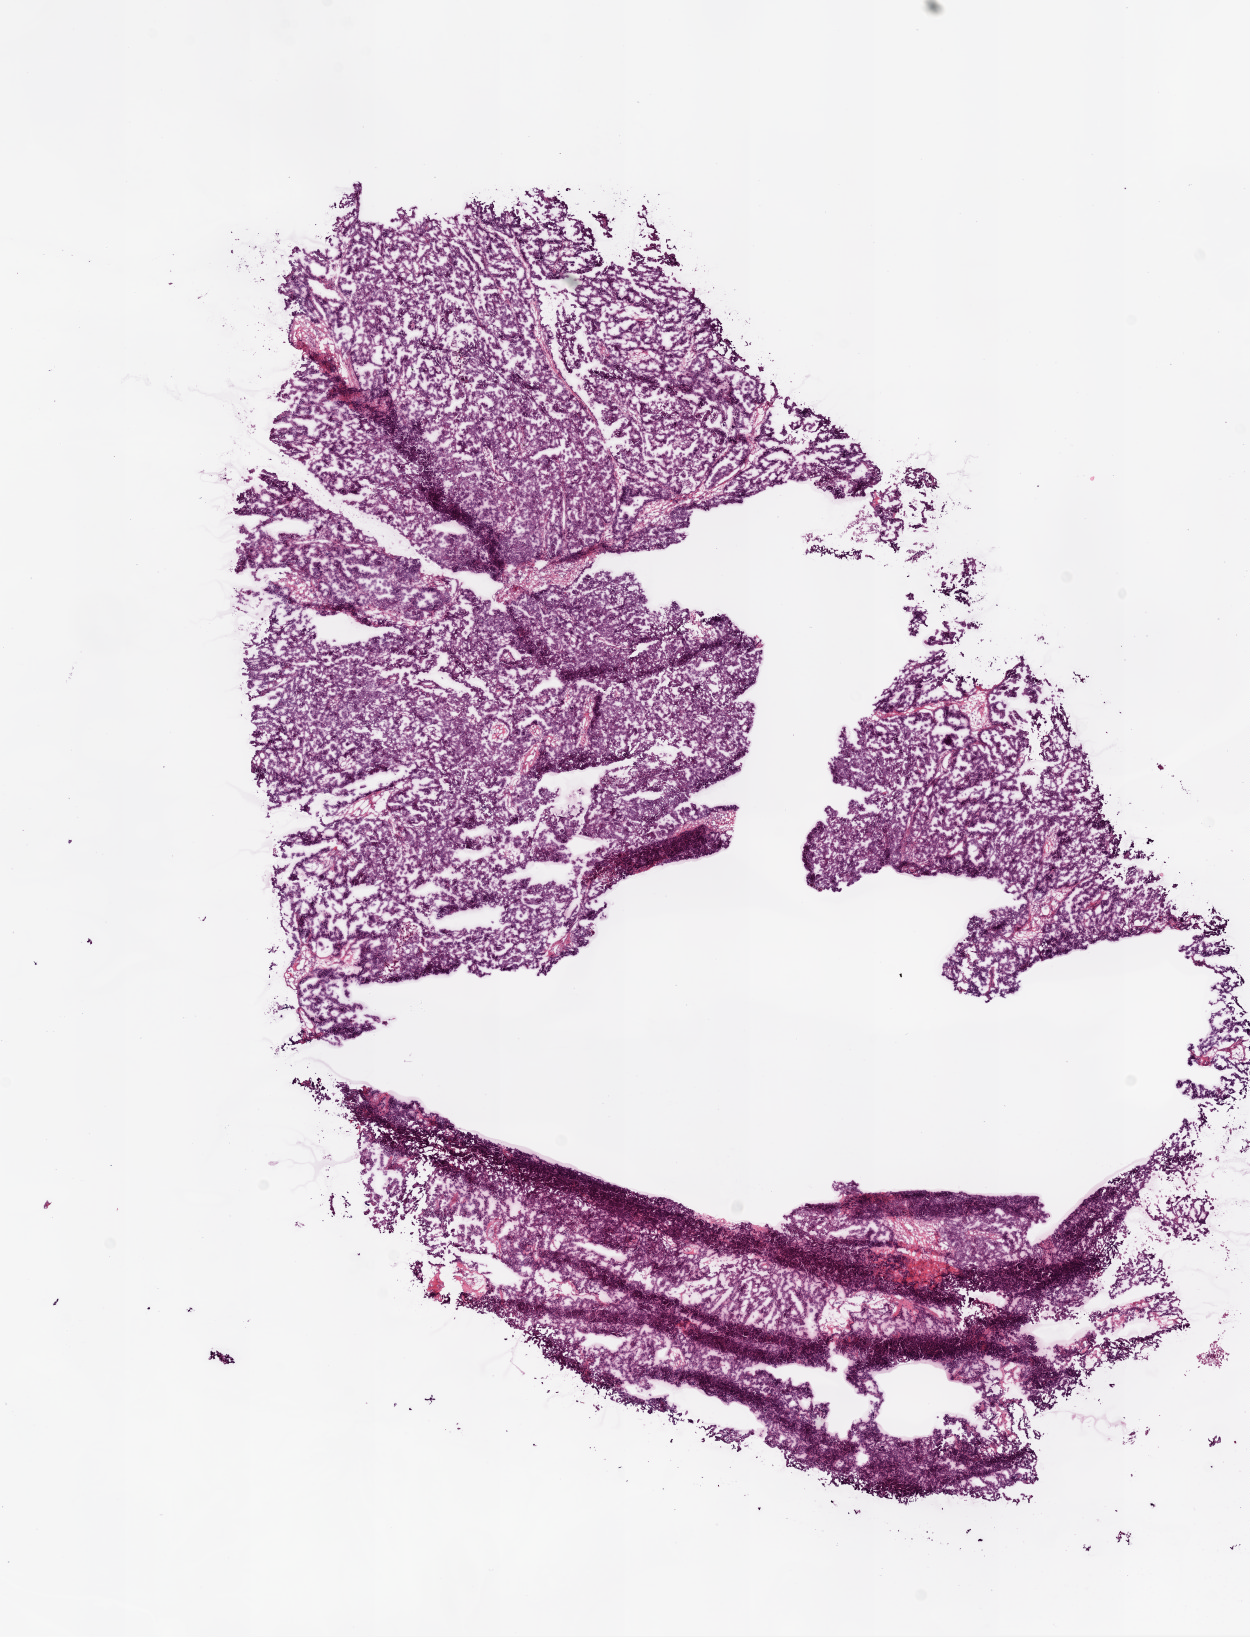
H&E whole-slide image — a low-resolution overview of the entire scanned area, about 10.0 x 13.1 mm, frozen section, sample: primary tumour, ovary. Female, age 61 years at initial diagnosis. Histologic grade: G2 (moderately differentiated). Composition of this section per pathologist review: tumour cells 95%, tumour nuclei 99%, normal cells 0%, stromal cells 5%, necrosis 0%.
• diagnosis: Serous cystadenocarcinoma, NOS
• FIGO stage: IV